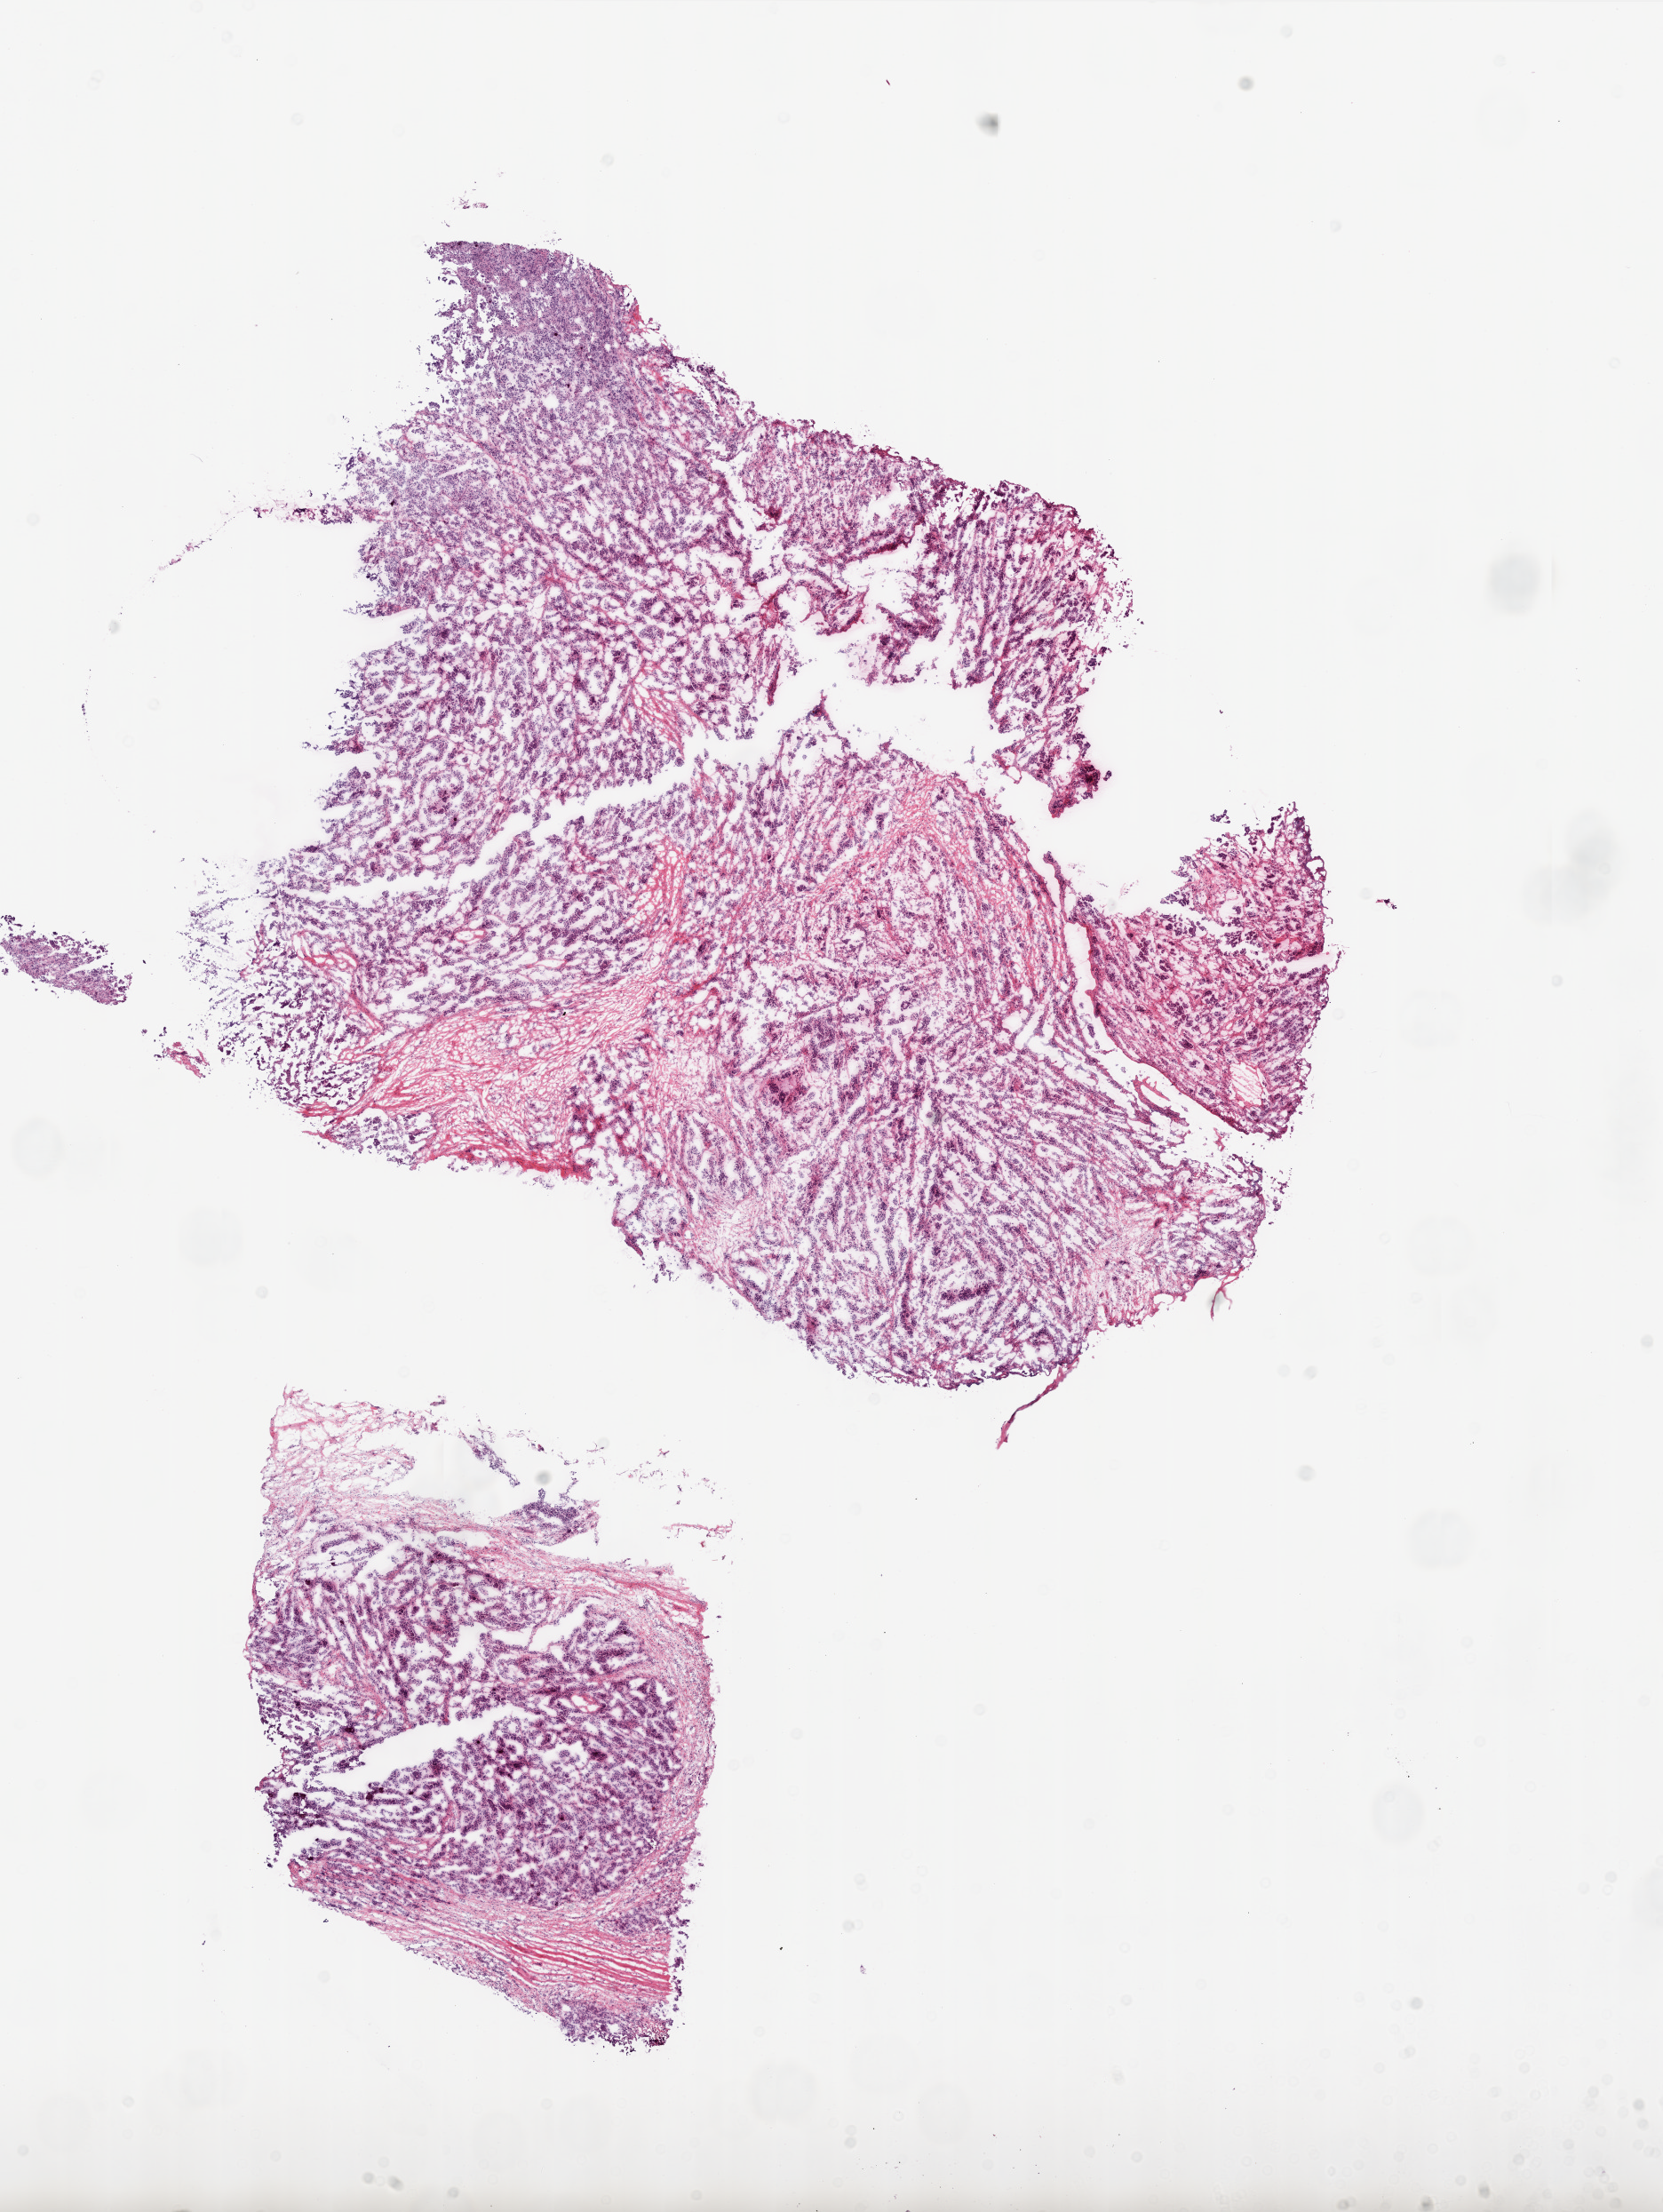
H&E-stained whole-slide image — whole scanned area (about 15.0 x 19.9 mm, acquisition: 20x scan) shown as a low-resolution overview, frozen section, primary tumour sample from the ovary. Female patient; age at initial diagnosis 52 years. Histologic grade: G3 (poorly differentiated). Pathologist review of this section (percent, as recorded): tumour cells 70%, tumour nuclei 80%, normal cells 0%, stromal cells 30%, necrosis 0%.
Diagnosis: Serous cystadenocarcinoma, NOS. FIGO stage: IIIC.